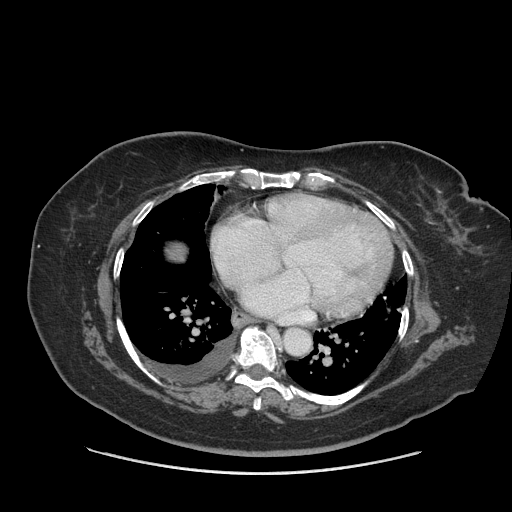
Contrast-enhanced abdominal CT (liver protocol), one axial slice; position 89 of 91 along the scan axis; reconstruction kernel STANDARD; 140 kVp; soft-tissue window (W 400 / L 40 HU); 2.5 mm slice thickness; 512 × 512 image matrix, field of view 420 × 420 mm. Case-level facts recorded for this patient, not image findings: diagnosis: hepatocellular carcinoma (patient treated with transarterial chemoembolisation; whether this scan precedes or follows treatment is not stated here); TNM stage (as recorded): Stage-I; Child-Pugh class: A.
Outlined on this slice (semi-automatically segmented with operator editing):
- liver parenchyma outside the tumour (the mass and vessels are separate outlines, so this box may not span the whole liver): box from (x=167, y=244) to (x=184, y=260) px